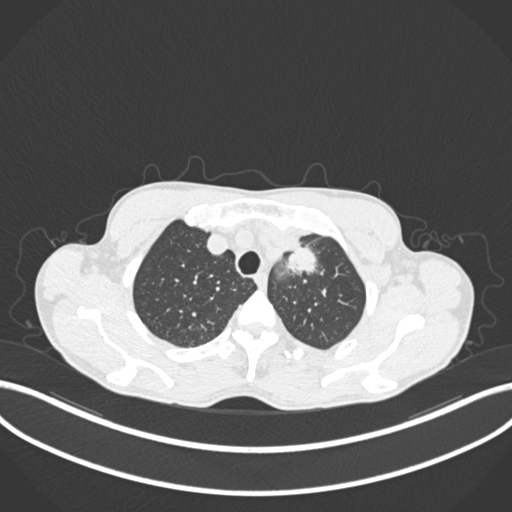
Chest CT, one axial slice. Position 171 of 211 along the scan axis. 120 kVp. Lung window (W 1500 / L -600 HU). 1 mm slice thickness. 512 × 512 image matrix. Patient: male, 58 years. Case-level facts recorded for this patient, not image findings: clinical TNM (as recorded): T1c N1 M0.
Annotated regions visible in this slice (rectangle marked by the reading radiologist):
- lung tumour (recorded histology: adenocarcinoma): bounding box [x1, y1, x2, y2] px = [282, 243, 321, 286]